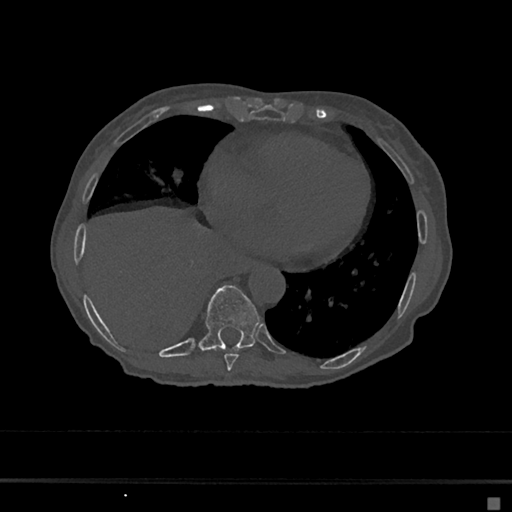
CT including the spine, one axial slice; position 290 of 797 along the scan axis; reconstruction kernel Br40s/3; 120 kVp; bone window (W 1800 / L 400 HU); 512 × 512 image matrix, field of view 360 × 360 mm. Patient: female, 68 years. From the clinical record (not read from this slice): primary cancer: renal.
Outlined on this slice (semi-automatic segmentation, software-assisted and operator-edited):
- T8 vertebra: bounding box <224,354,239,371> (left, top, right, bottom; pixels)
- T9 vertebra: <198,285,260,352>